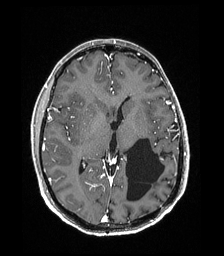
Brain MRI from a brain-tumour surgery series, one axial slice. Slice 96 of 192 in the series (ordered by position). T1-weighted post-contrast. 1 mm slice thickness. 224 × 256 image matrix, field of view 224 × 256 mm. From the clinical record (not read from this slice): histopathology: Low grade glioma; IDH mutation: no; tumour location: Left Parieto-Occipital Intraventricular.
Outlined on this slice (manually delineated by an expert):
- previous resection cavity: box from (x=126, y=138) to (x=164, y=201) px